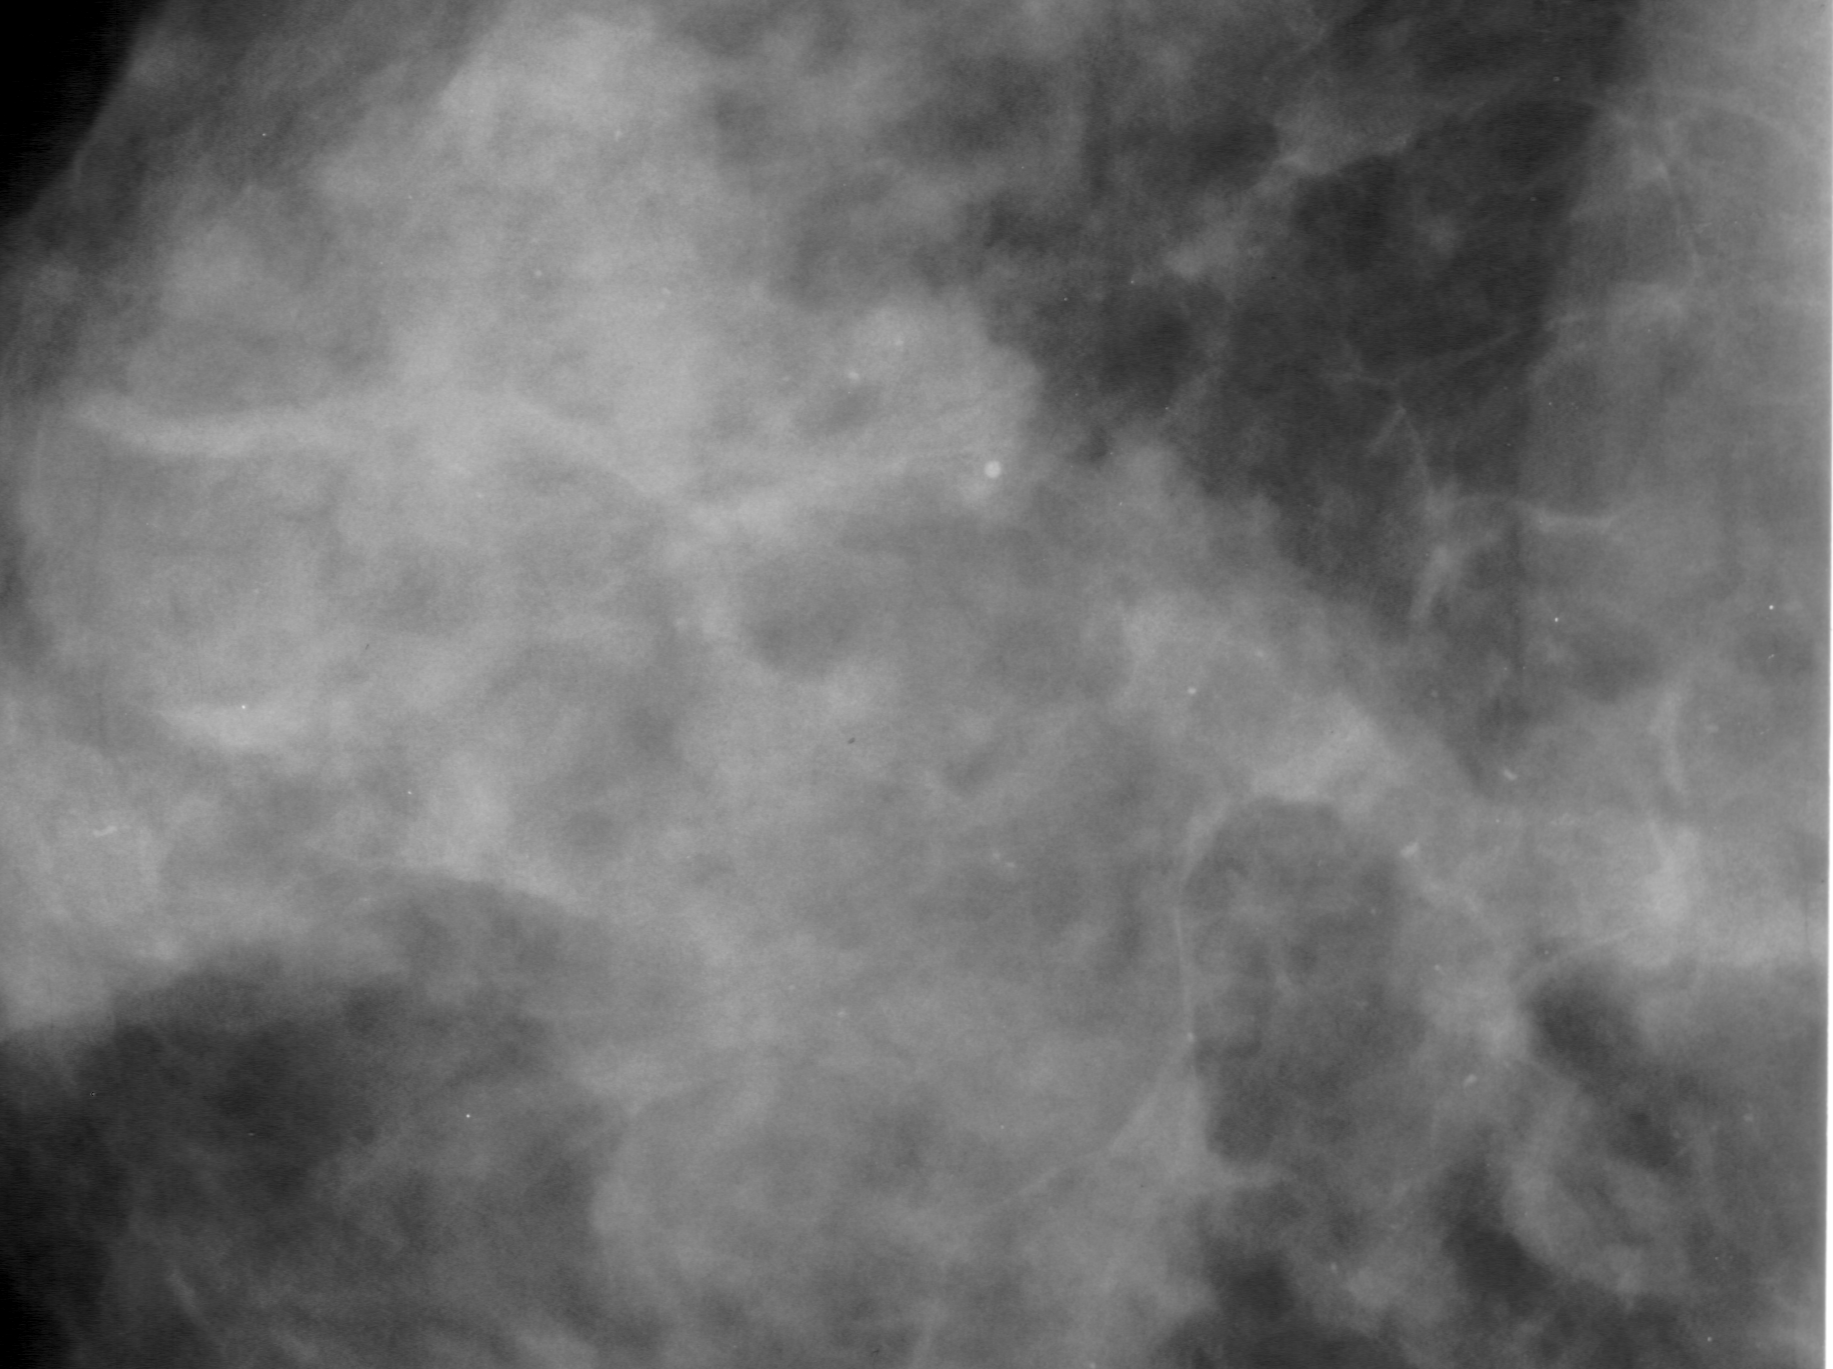
Cropped region of a digitized screen-film mammogram centred on a radiologist-marked abnormality; left breast; CC view; BI-RADS breast density category 3 (scale 1–4).
Marked abnormality: calcifications, morphology pleomorphic, distribution segmental; BI-RADS assessment category 4; subtlety rating 3 on a 1 (subtle) to 5 (obvious) scale; pathology (as recorded): malignant.